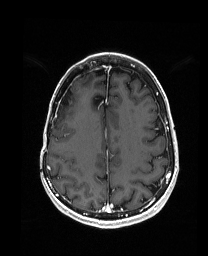
Brain MRI from a brain-tumour surgery series, one axial slice; position 59 of 192 along the scan axis; T1-weighted post-contrast; 1 mm slice thickness; 208 × 256 image matrix, field of view 203 × 250 mm. From the clinical record (not read from this slice): histopathology: Metastatic Carcinoma from Breast primary; tumour location: Right Frontal.
Annotated regions visible in this slice (manually delineated by an expert):
- previous resection cavity: bounding box <61,86,72,106> (left, top, right, bottom; pixels)